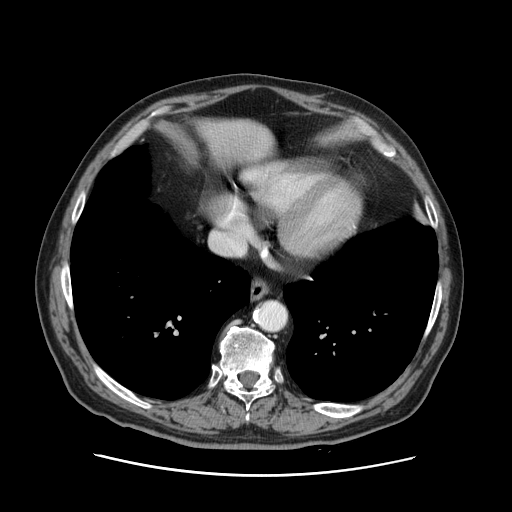
Contrast-enhanced abdominal CT, one axial slice; position 123 of 141 along the scan axis; 120 kVp; intravenous contrast given; soft-tissue window (W 400 / L 40 HU); 2.5 mm slice thickness; 512 × 512 image matrix, field of view 395 × 395 mm. Male patient, age 72 years. Case-level facts recorded for this patient, not image findings: diagnosis: colorectal cancer liver metastases, imaged before liver resection; multiple liver metastases: yes; largest metastasis: 5.4 cm; disease in both lobes: yes.
Annotated regions visible in this slice (outlined manually by an expert reader):
- liver: bounding box (x1, y1, x2, y2) in pixels: (197, 119, 274, 163)
- planned liver remnant (the part of the liver to remain after resection): (198, 119, 274, 164)